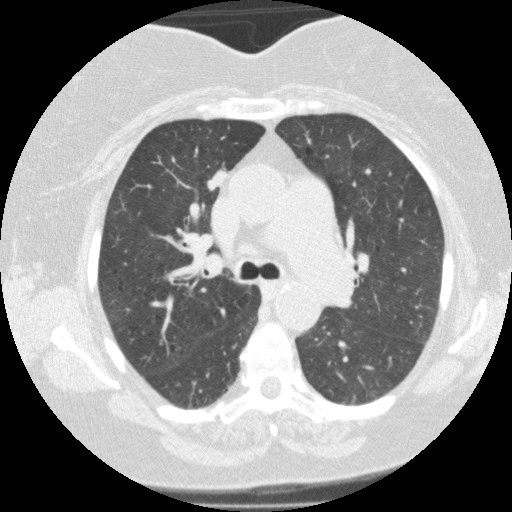
Low-dose screening chest CT, axial slice, third annual screen, lung window (W 1500 / L -600 HU), 2 mm slice thickness, standard (soft-tissue) reconstruction kernel (FC01). Female, age 62 years at enrolment. Current smoker at enrolment.
- Expert reader's lesion annotation, box from (x=190, y=159) to (x=236, y=200) px.
- The screening reader recorded 5 non-calcified nodules or masses ≥4 mm on this exam (right upper lobe, right lower lobe, right lower lobe, right lower lobe, right lower lobe); which of them this box marks is not recorded.